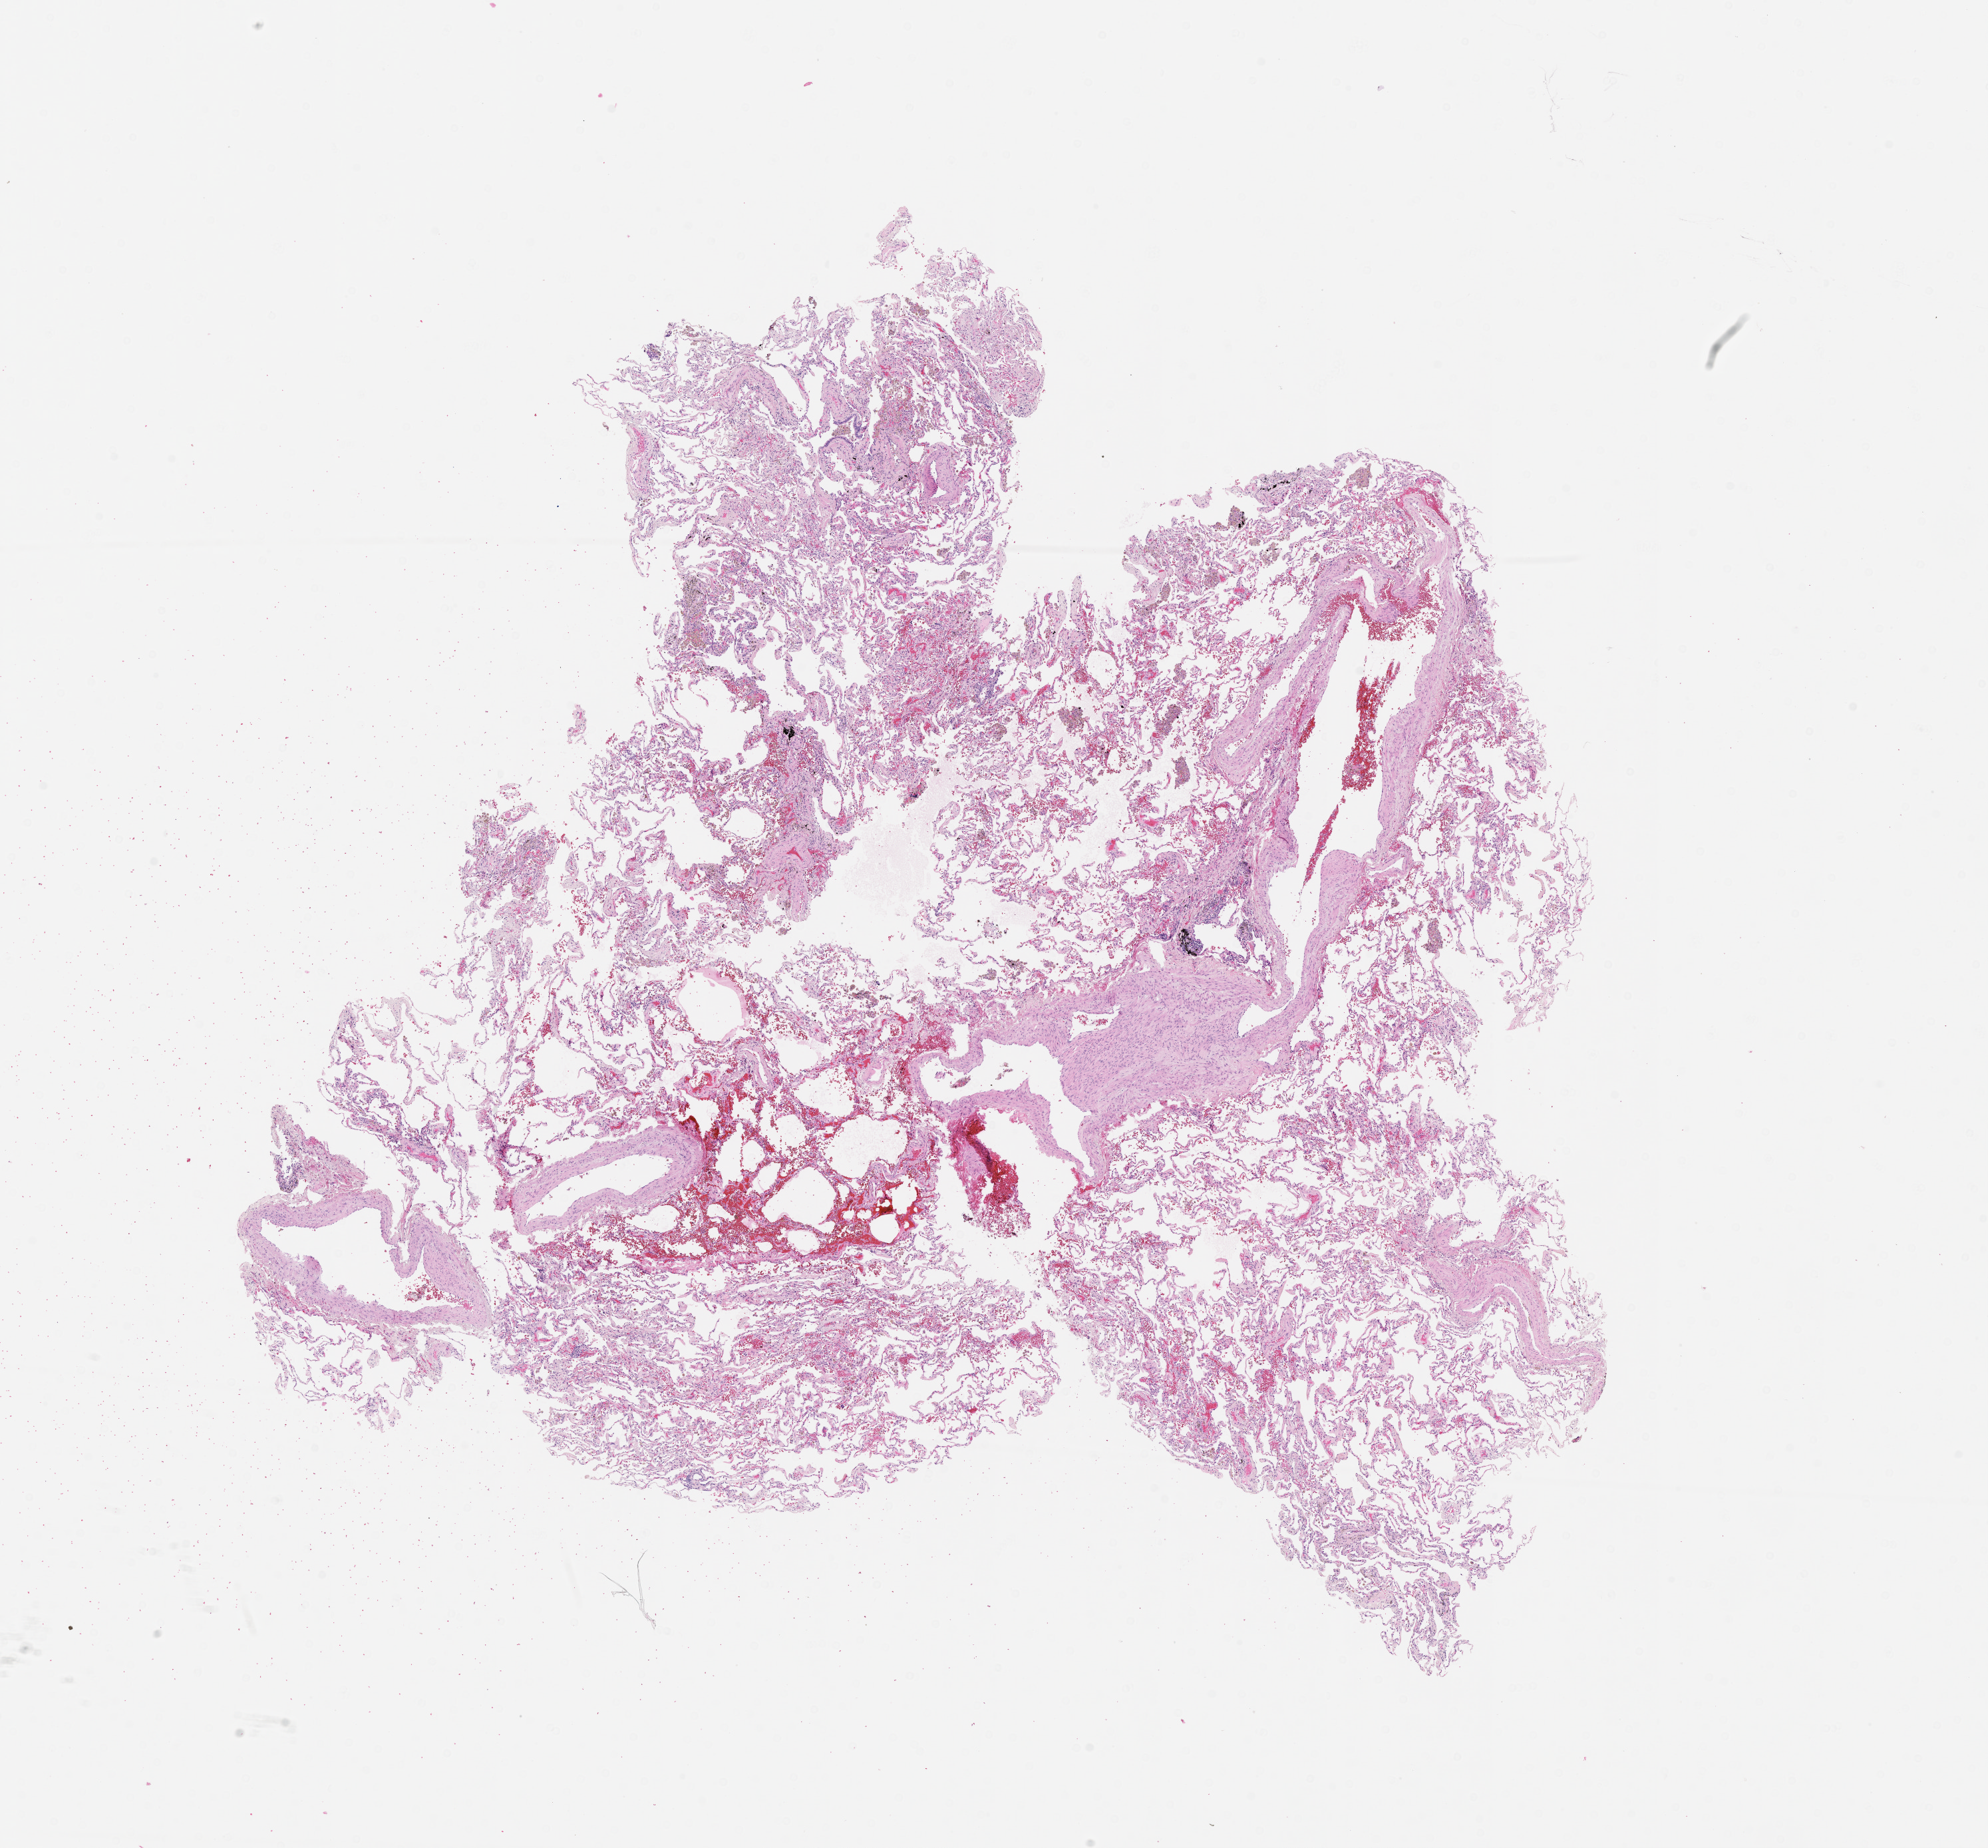
Whole-slide histology image, H&E — whole scanned area (about 12.0 x 11.2 mm, acquisition: 20x scan) shown as a low-resolution overview. Normal (non-tumour) tissue sample, lung. 69-year-old female patient.
This section: normal (non-tumour) tissue from the same patient. Patient diagnosis (cohort enrolment): squamous cell carcinoma (lung).